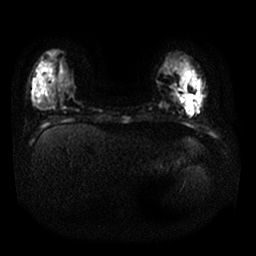
Breast MRI, one axial slice. Position 2 of 25 along the scan axis. Diffusion-weighted series; image 2 of 4 stored at this slice position (different b-values; order by instance number). 1.5 T. 4 mm slice thickness. 256 × 256 image matrix, field of view 330 × 330 mm. Female patient.
Structures marked on this image (outlined manually by an expert reader):
- tumour on diffusion-weighted imaging: bounding box [x1, y1, x2, y2] px = [185, 94, 194, 108]